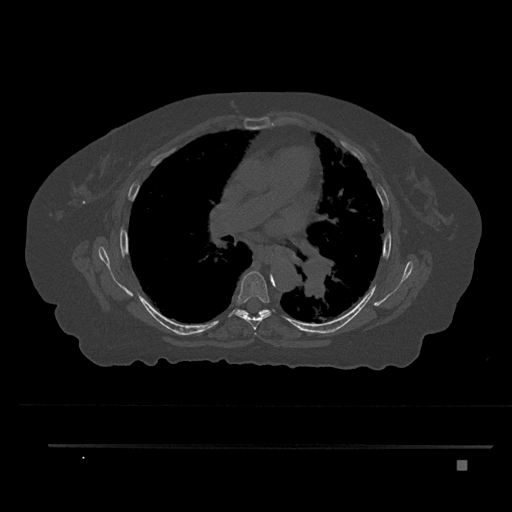
CT including the spine, one axial slice; slice 519 of 797 in the series (ordered by position); bone window (W 1800 / L 400 HU); 0.5 mm slice thickness; 512 × 512 image matrix, field of view 437 × 437 mm. Female patient, age 76 years. Case-level facts recorded for this patient, not image findings: primary cancer: lung; vertebrae with lytic lesions (as recorded): T11, L3.
Structures marked on this image (semi-automatically segmented with operator editing):
- T6 vertebra: bounding box <235,271,271,330> (left, top, right, bottom; pixels)
- T7 vertebra: <237,309,269,317>